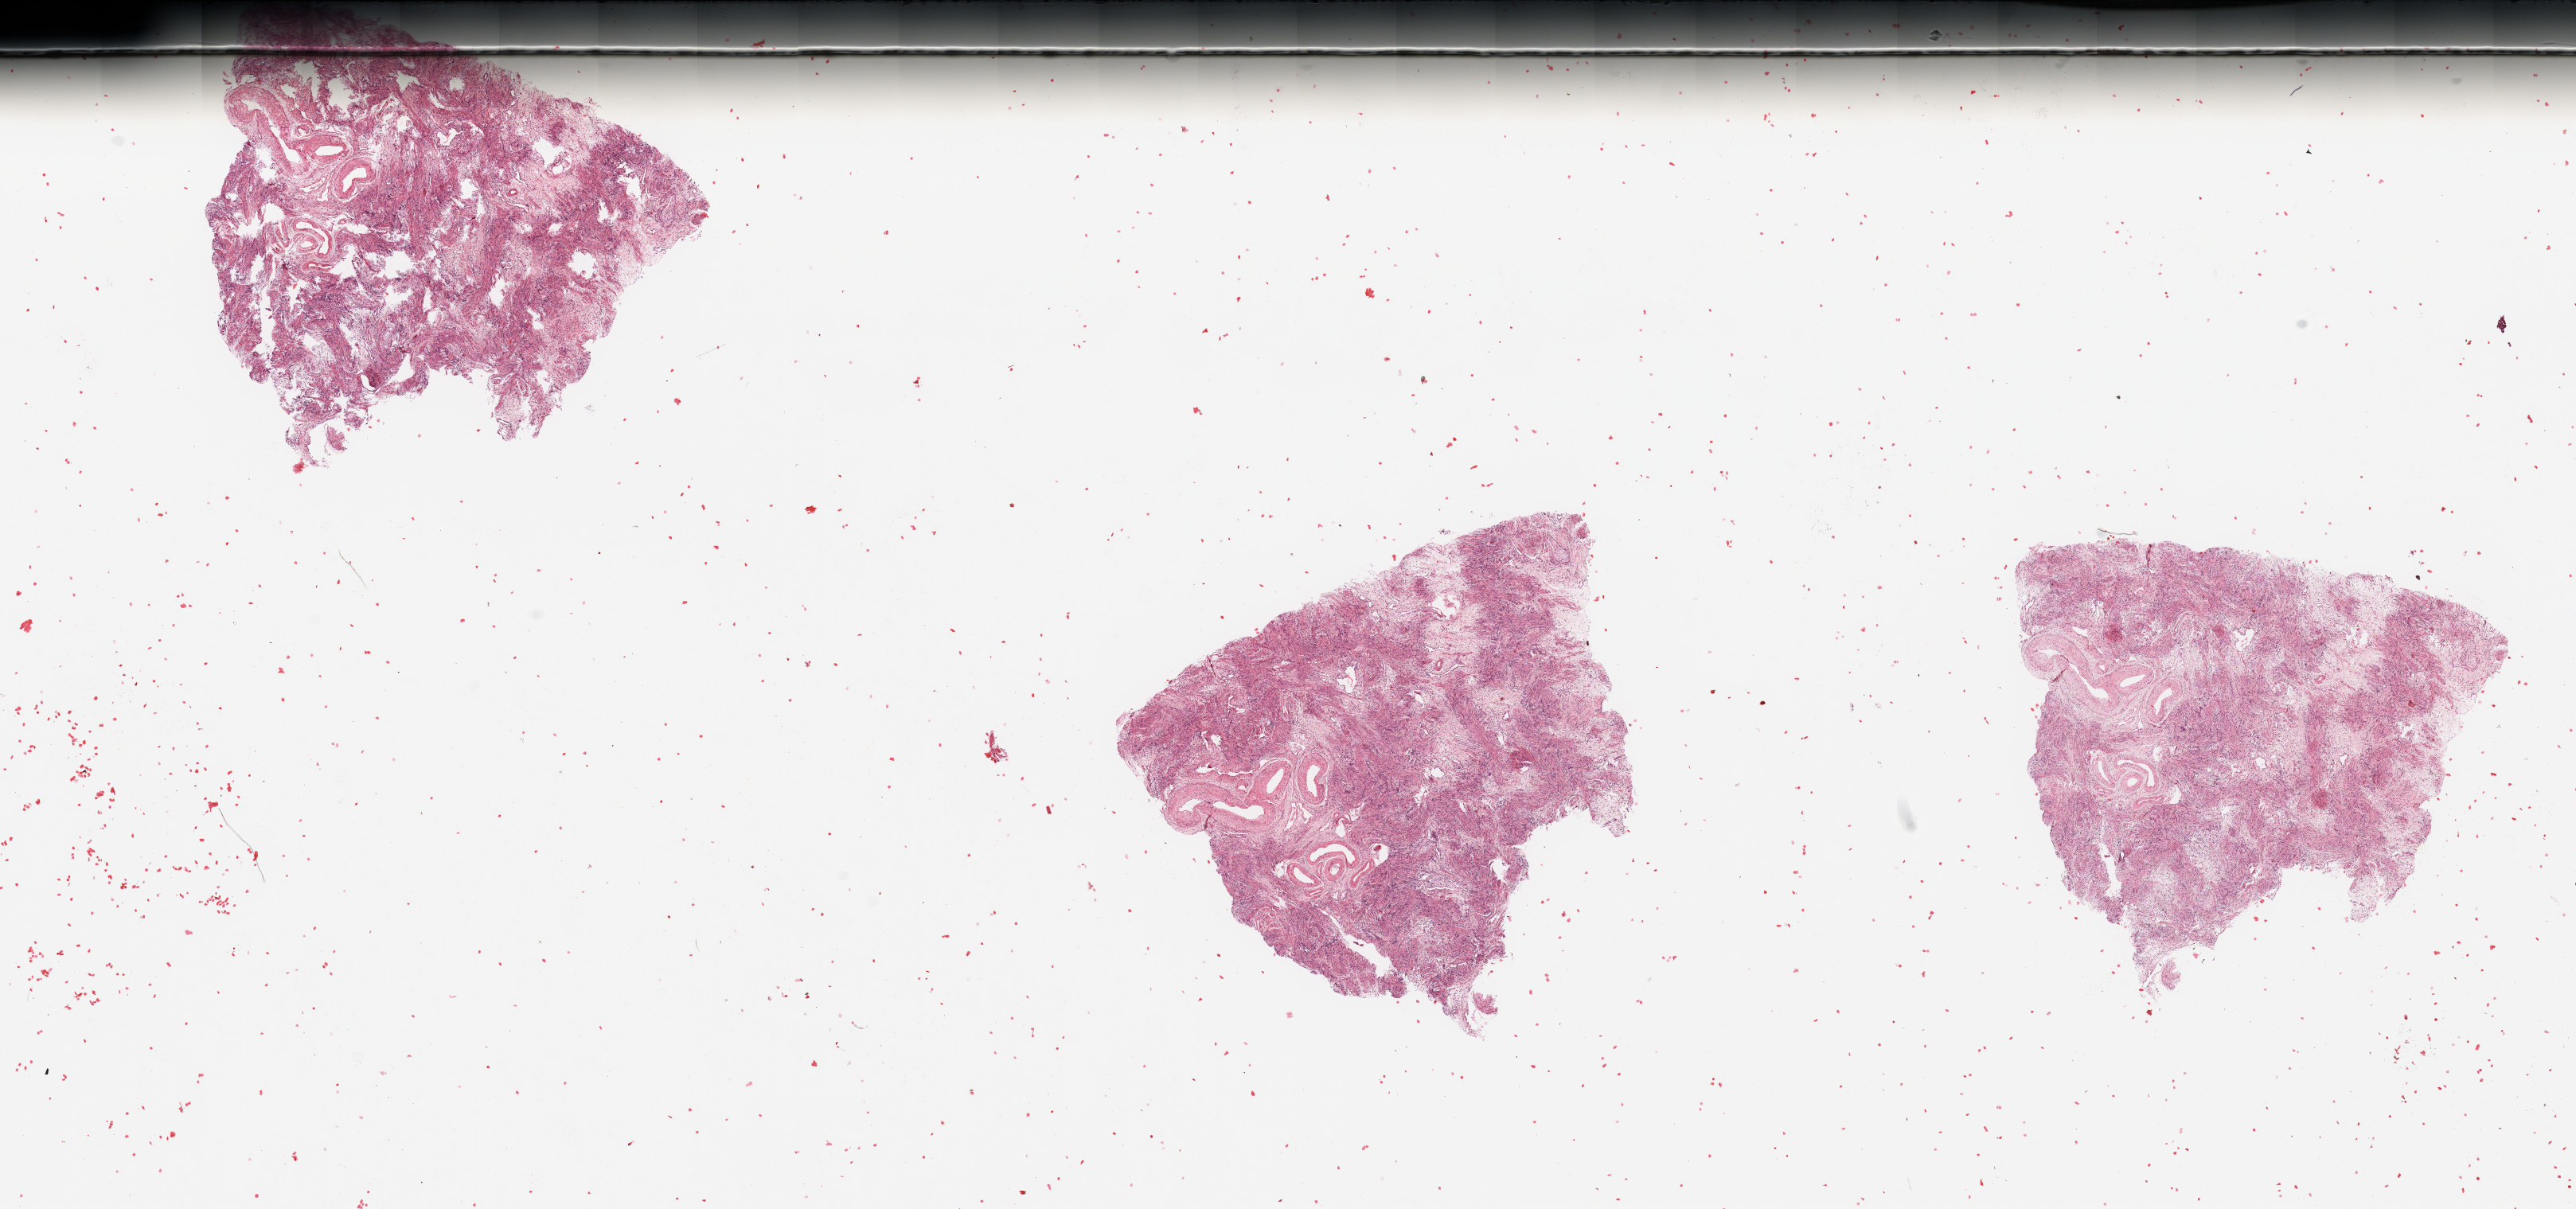
Whole-slide histology image, H&E-stained, whole scanned area (about 25.6 x 12.0 mm) shown as a low-resolution overview. Normal (non-tumour) tissue sample, uterus. Patient: female, age 69 years.
- this section: normal (non-tumour) tissue from the same patient
- patient diagnosis: Endometrioid adenocarcinoma, NOS